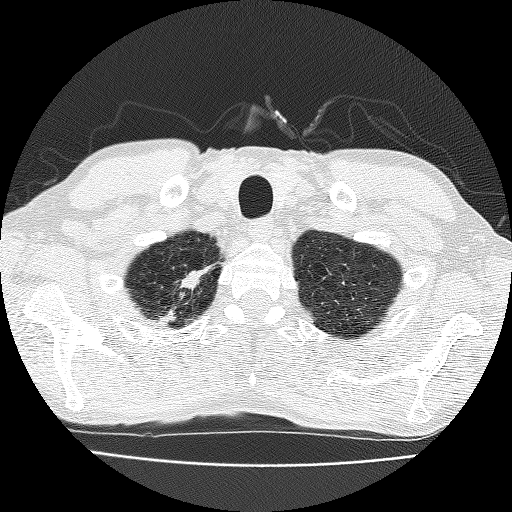
Low-dose screening chest CT, one axial slice; position 161 of 185 along the scan axis; reconstruction kernel FC51; 120 kVp; lung window (W 1500 / L -600 HU); 2 mm slice thickness; 512 × 512 image matrix, field of view 322 × 322 mm.
Structures marked on this image (manually delineated by an expert):
- lesion 1 (nodule, upper lobe of right lung): bounding box (x1, y1, x2, y2) in pixels: (181, 269, 207, 290)